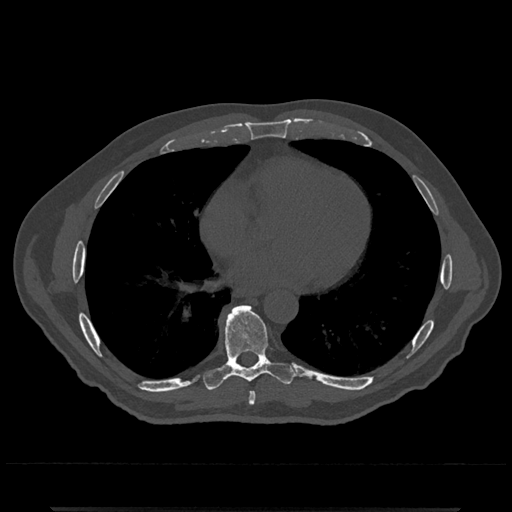
CT including the spine, one axial slice; slice 672 of 797 in the series (ordered by position); reconstruction kernel Br40s/3; 120 kVp; bone window (W 1800 / L 400 HU); 512 × 512 image matrix. Male patient, age 67 years. From the clinical record (not read from this slice): primary cancer: prostate.
Outlined on this slice (semi-automatically segmented with operator editing):
- T7 vertebra: bounding box [x1, y1, x2, y2] px = [248, 391, 256, 406]
- T8 vertebra: [203, 305, 295, 390]